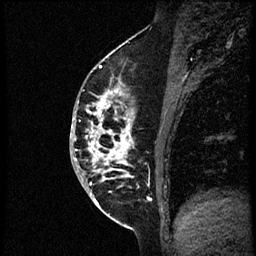
Breast MRI (dynamic contrast-enhanced), one sagittal slice. Position 27 of 56 along the scan axis. Dynamic contrast-enhanced study with each time point stored as its own series, time point 2 of 3 at this slice position (early post-contrast, ordered by acquisition time). 1.5 T. TE 4.2 ms, TR 21.3 ms. 2 mm slice thickness. 256 × 256 image matrix, field of view 200 × 200 mm. Female patient, age 41 years. Case-level facts recorded for this patient, not image findings: setting: breast cancer imaged before/during neoadjuvant chemotherapy; receptor status: HER2-positive.
Annotated regions visible in this slice (semi-automatically segmented with operator editing):
- analysis volume of interest (the breast-tissue region the enhancement analysis was run in; not a lesion): bounding box [x1, y1, x2, y2] px = [84, 73, 177, 205]
- tumour enhancement mask (voxels above the 100 % enhancement threshold inside the analysis volume of interest): [86, 77, 150, 205]